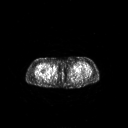
FDG PET of an extremity soft-tissue mass (from a PET/CT study), one axial slice. Slice 244 of 311 in the series (ordered by position). 128 × 128 image matrix, field of view 700 × 700 mm. Patient: female, 78 years. From the clinical record (not read from this slice): histological type: leiomyosarcoma; grade: intermediate; site of the primary tumour: parascapusular.
Structures marked on this image (expert contour drawn on MRI and transferred to this co-registered scan by the dataset authors):
- gross tumour volume including surrounding oedema: bounding box [x1, y1, x2, y2] px = [53, 65, 58, 70]
- gross tumour volume (mass): [53, 65, 57, 69]